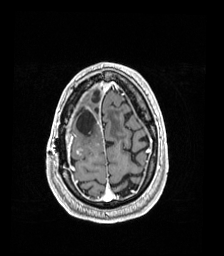
Brain MRI from a brain-tumour surgery series, one axial slice; position 35 of 192 along the scan axis; T1-weighted post-contrast; 1 mm slice thickness; 224 × 256 image matrix. From the clinical record (not read from this slice): histopathology: Astrocytoma; WHO grade: 4; IDH mutation: yes; tumour location: Right Frontal.
Structures marked on this image (expert manual segmentation):
- previous resection cavity: bounding box [x1, y1, x2, y2] px = [76, 110, 96, 135]
- tumour: [76, 146, 85, 156]